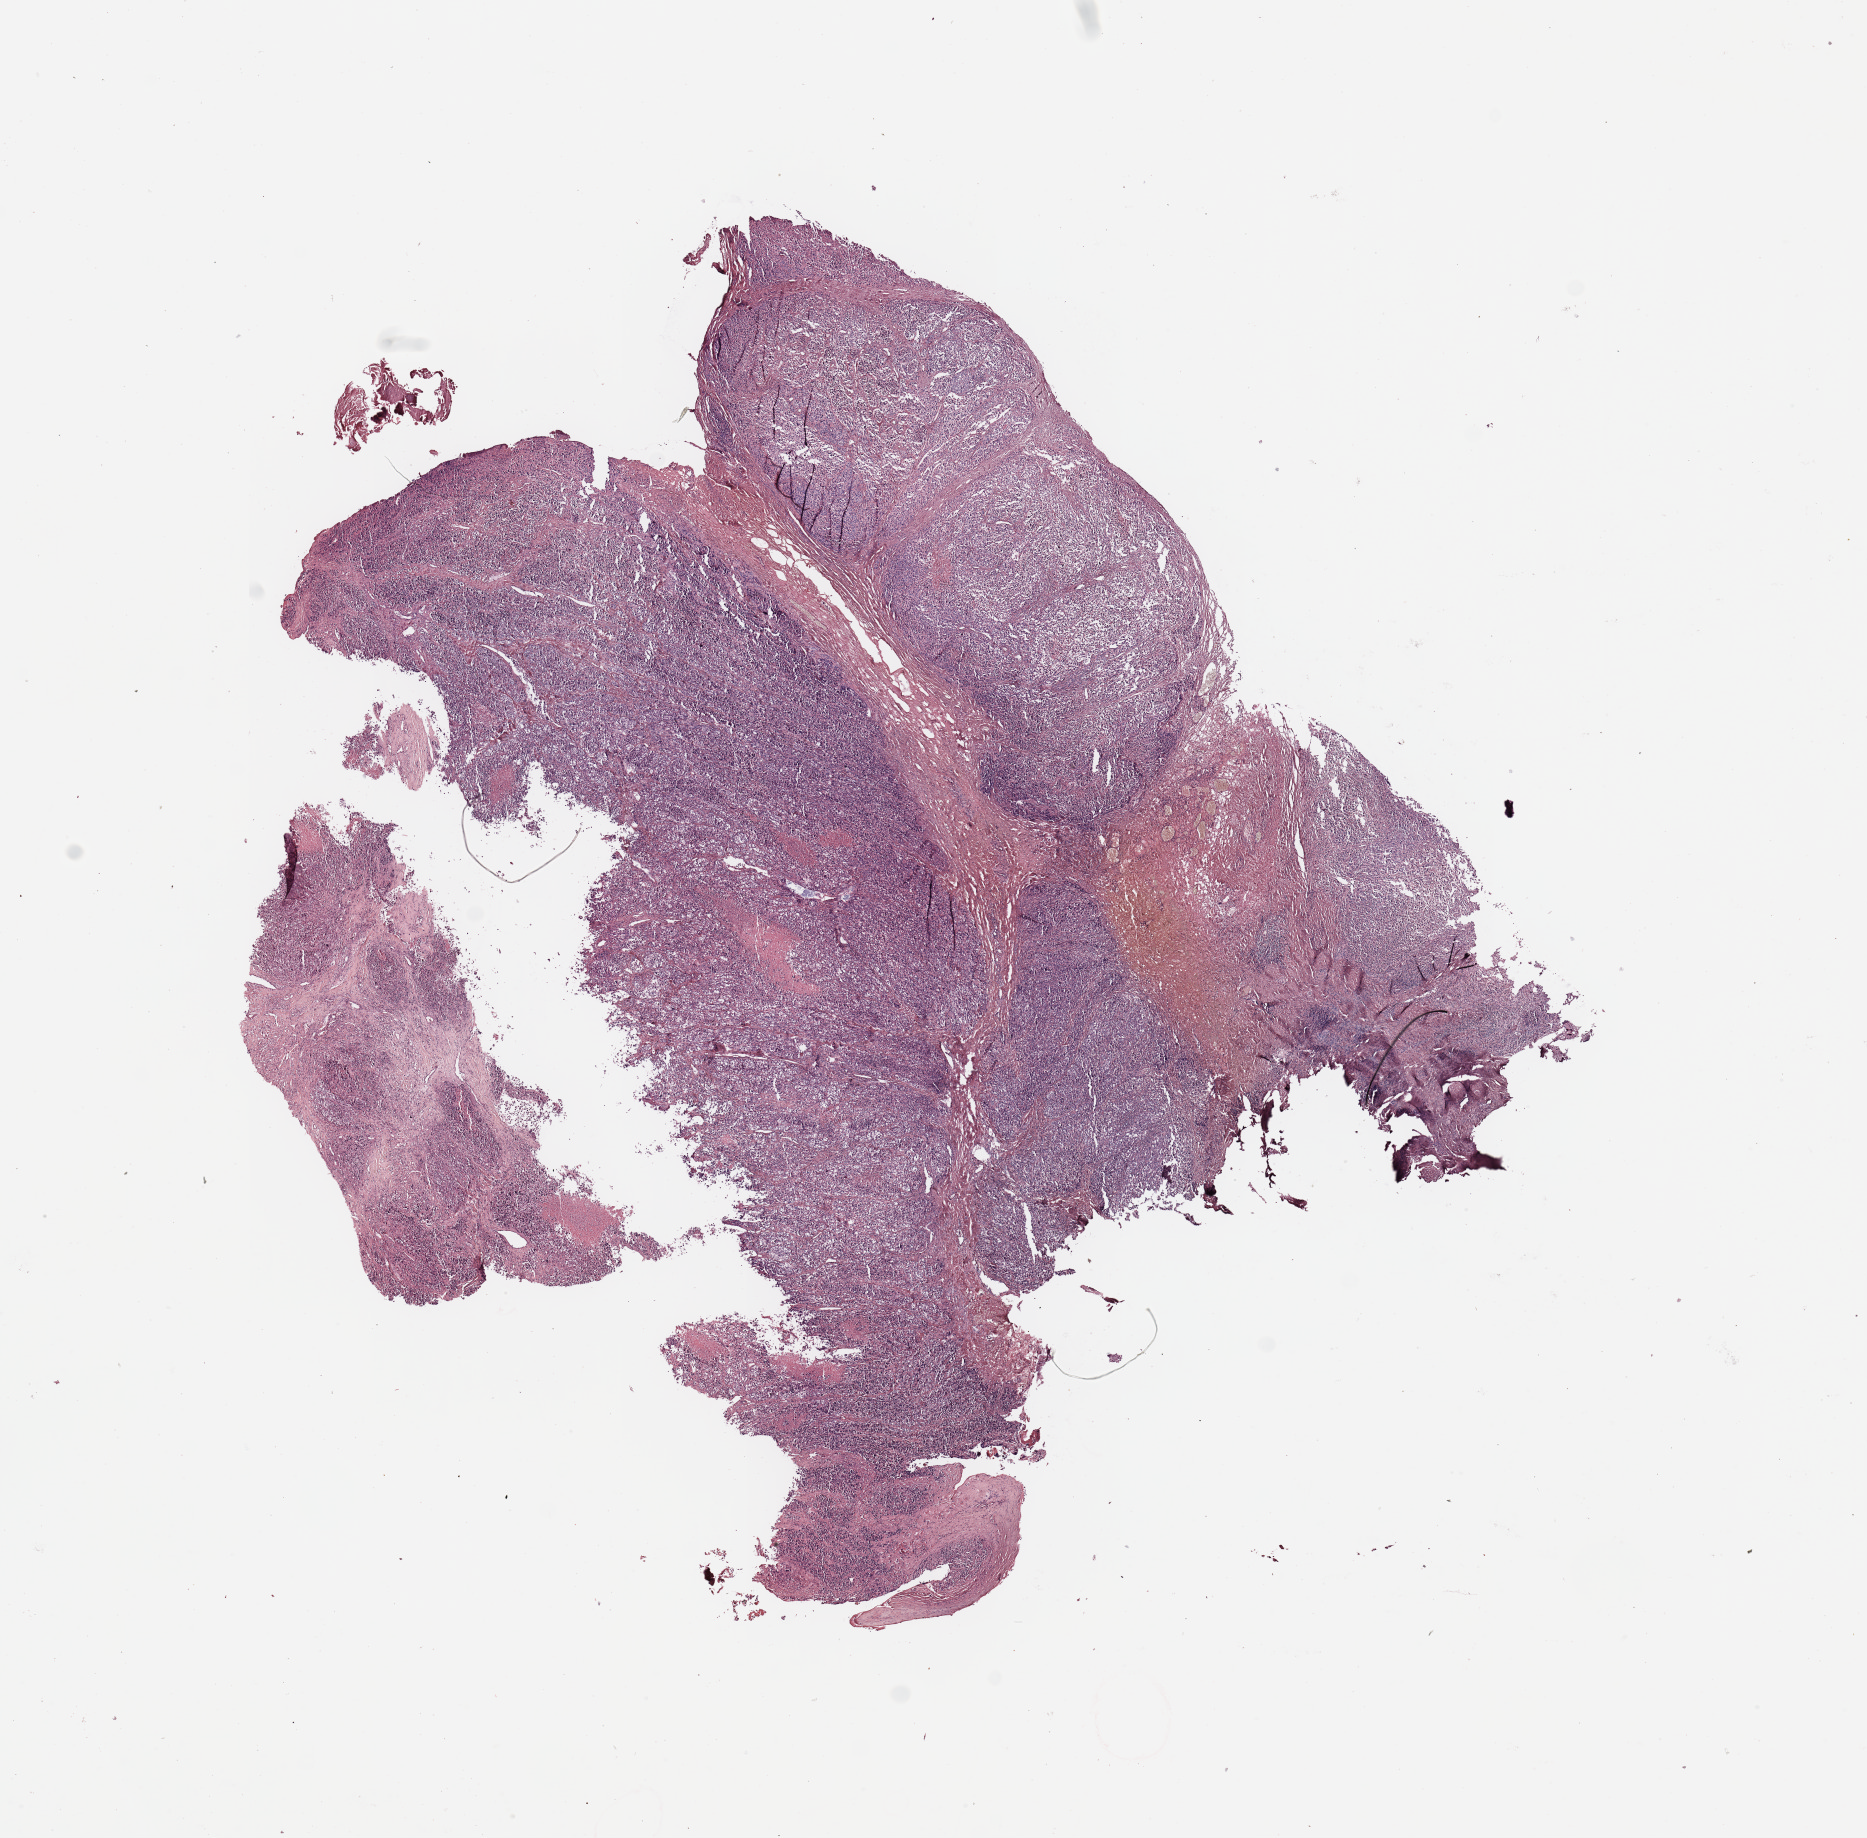
H&E-stained whole-slide image, whole scanned area (about 14.8 x 14.5 mm, acquisition: 20x scan) shown as a low-resolution overview. Tumour tissue sample, sampled site: trunk. Patient: male, age 76 years. Pathologist review of this section (percent, as recorded): tumour nuclei 95%, necrosis 10%.
* this section: metastatic tumour tissue
* patient diagnosis: Malignant melanoma, NOS